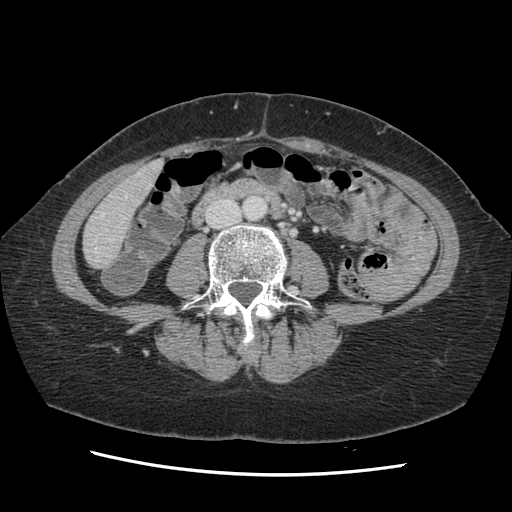
Contrast-enhanced abdominal CT, one axial slice; slice 27 of 141 in the series (ordered by position); 120 kVp; soft-tissue window (W 400 / L 40 HU); 2.5 mm slice thickness; 512 × 512 image matrix. Female patient, age 61 years. Case-level facts recorded for this patient, not image findings: diagnosis: colorectal cancer liver metastases, imaged before liver resection; multiple liver metastases: no; largest metastasis: 2.4 cm; disease in both lobes: no.
Structures marked on this image (outlined manually by an expert reader):
- hepatic veins: box from (x=94, y=173) to (x=150, y=253) px
- liver: (x=84, y=162)–(x=163, y=268)
- planned liver remnant (the part of the liver to remain after resection): (x=84, y=162)–(x=163, y=268)